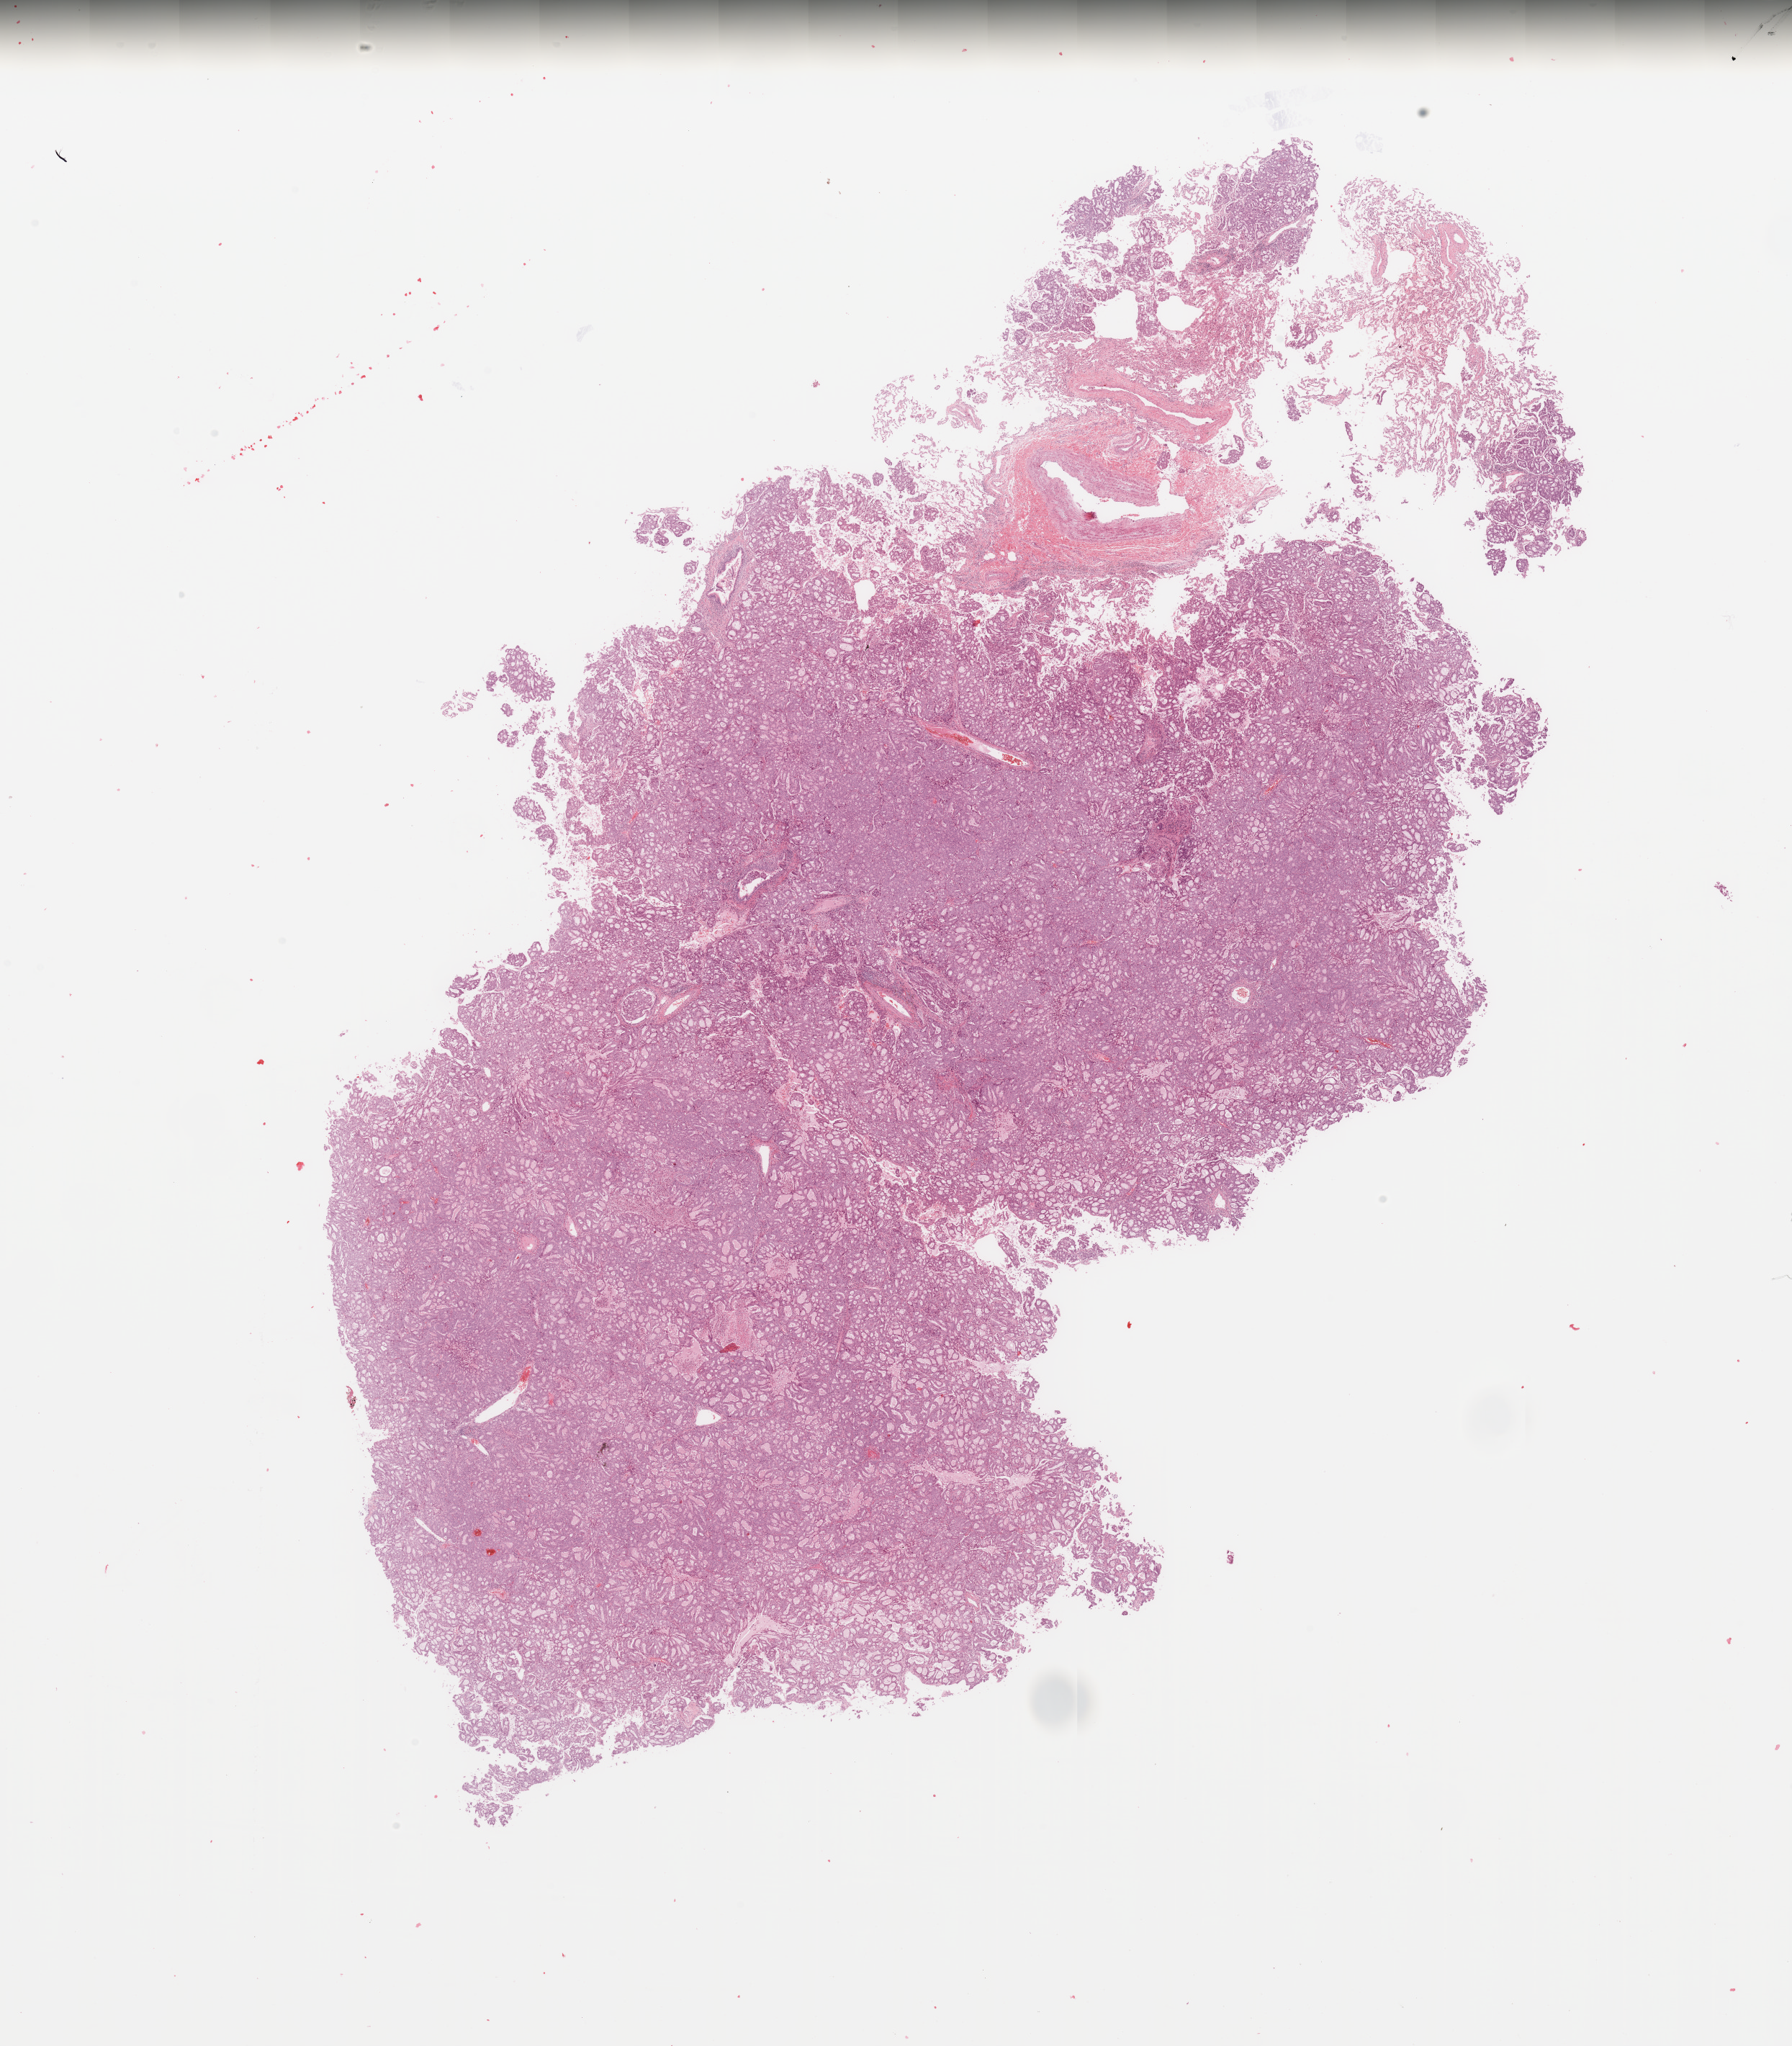
Whole-slide histology image, Hematoxylin and eosin (H&E) stained, whole scanned area (about 19.7 x 22.5 mm) shown as a low-resolution overview; tumour tissue sample, sampled site: lung. Male, 58 y/o. Histologic grade: G2 (moderately differentiated). Pathologist review of this section (percent, as recorded): tumour nuclei 85%, necrosis 1%.
Histologic diagnosis: Adenocarcinoma, NOS. Primary tumour site (as recorded): left lower lobe. AJCC pathologic stage: IB.